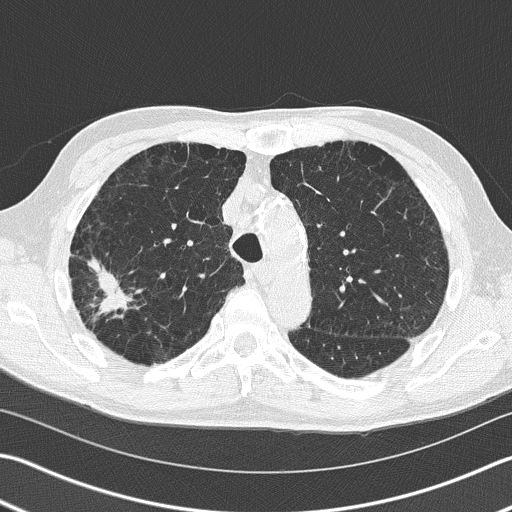
Low-dose screening chest CT, axial slice; baseline screening round; lung window (W 1500 / L -600 HU); 2 mm slice thickness; slice 51 of 163 in the series; 512 × 512 image matrix. Male, age 66 years at enrolment. Current smoker at enrolment.
Expert-annotated lung lesion, bounding box (x1, y1, x2, y2) in pixels: (64, 245, 137, 339). The exam's reader record, not a measurement of the box and not confirmed to be the same lesion: non-calcified nodule or mass ≥4 mm, right upper lobe, 39 × 23 mm, spiculated (stellate) margins, soft tissue attenuation. Participant outcome: lung cancer diagnosed 36 days after this screen — squamous cell carcinoma, NOS, right upper lobe, poorly differentiated (G3), stage IB (AJCC 6th edition), 23 mm at pathology.